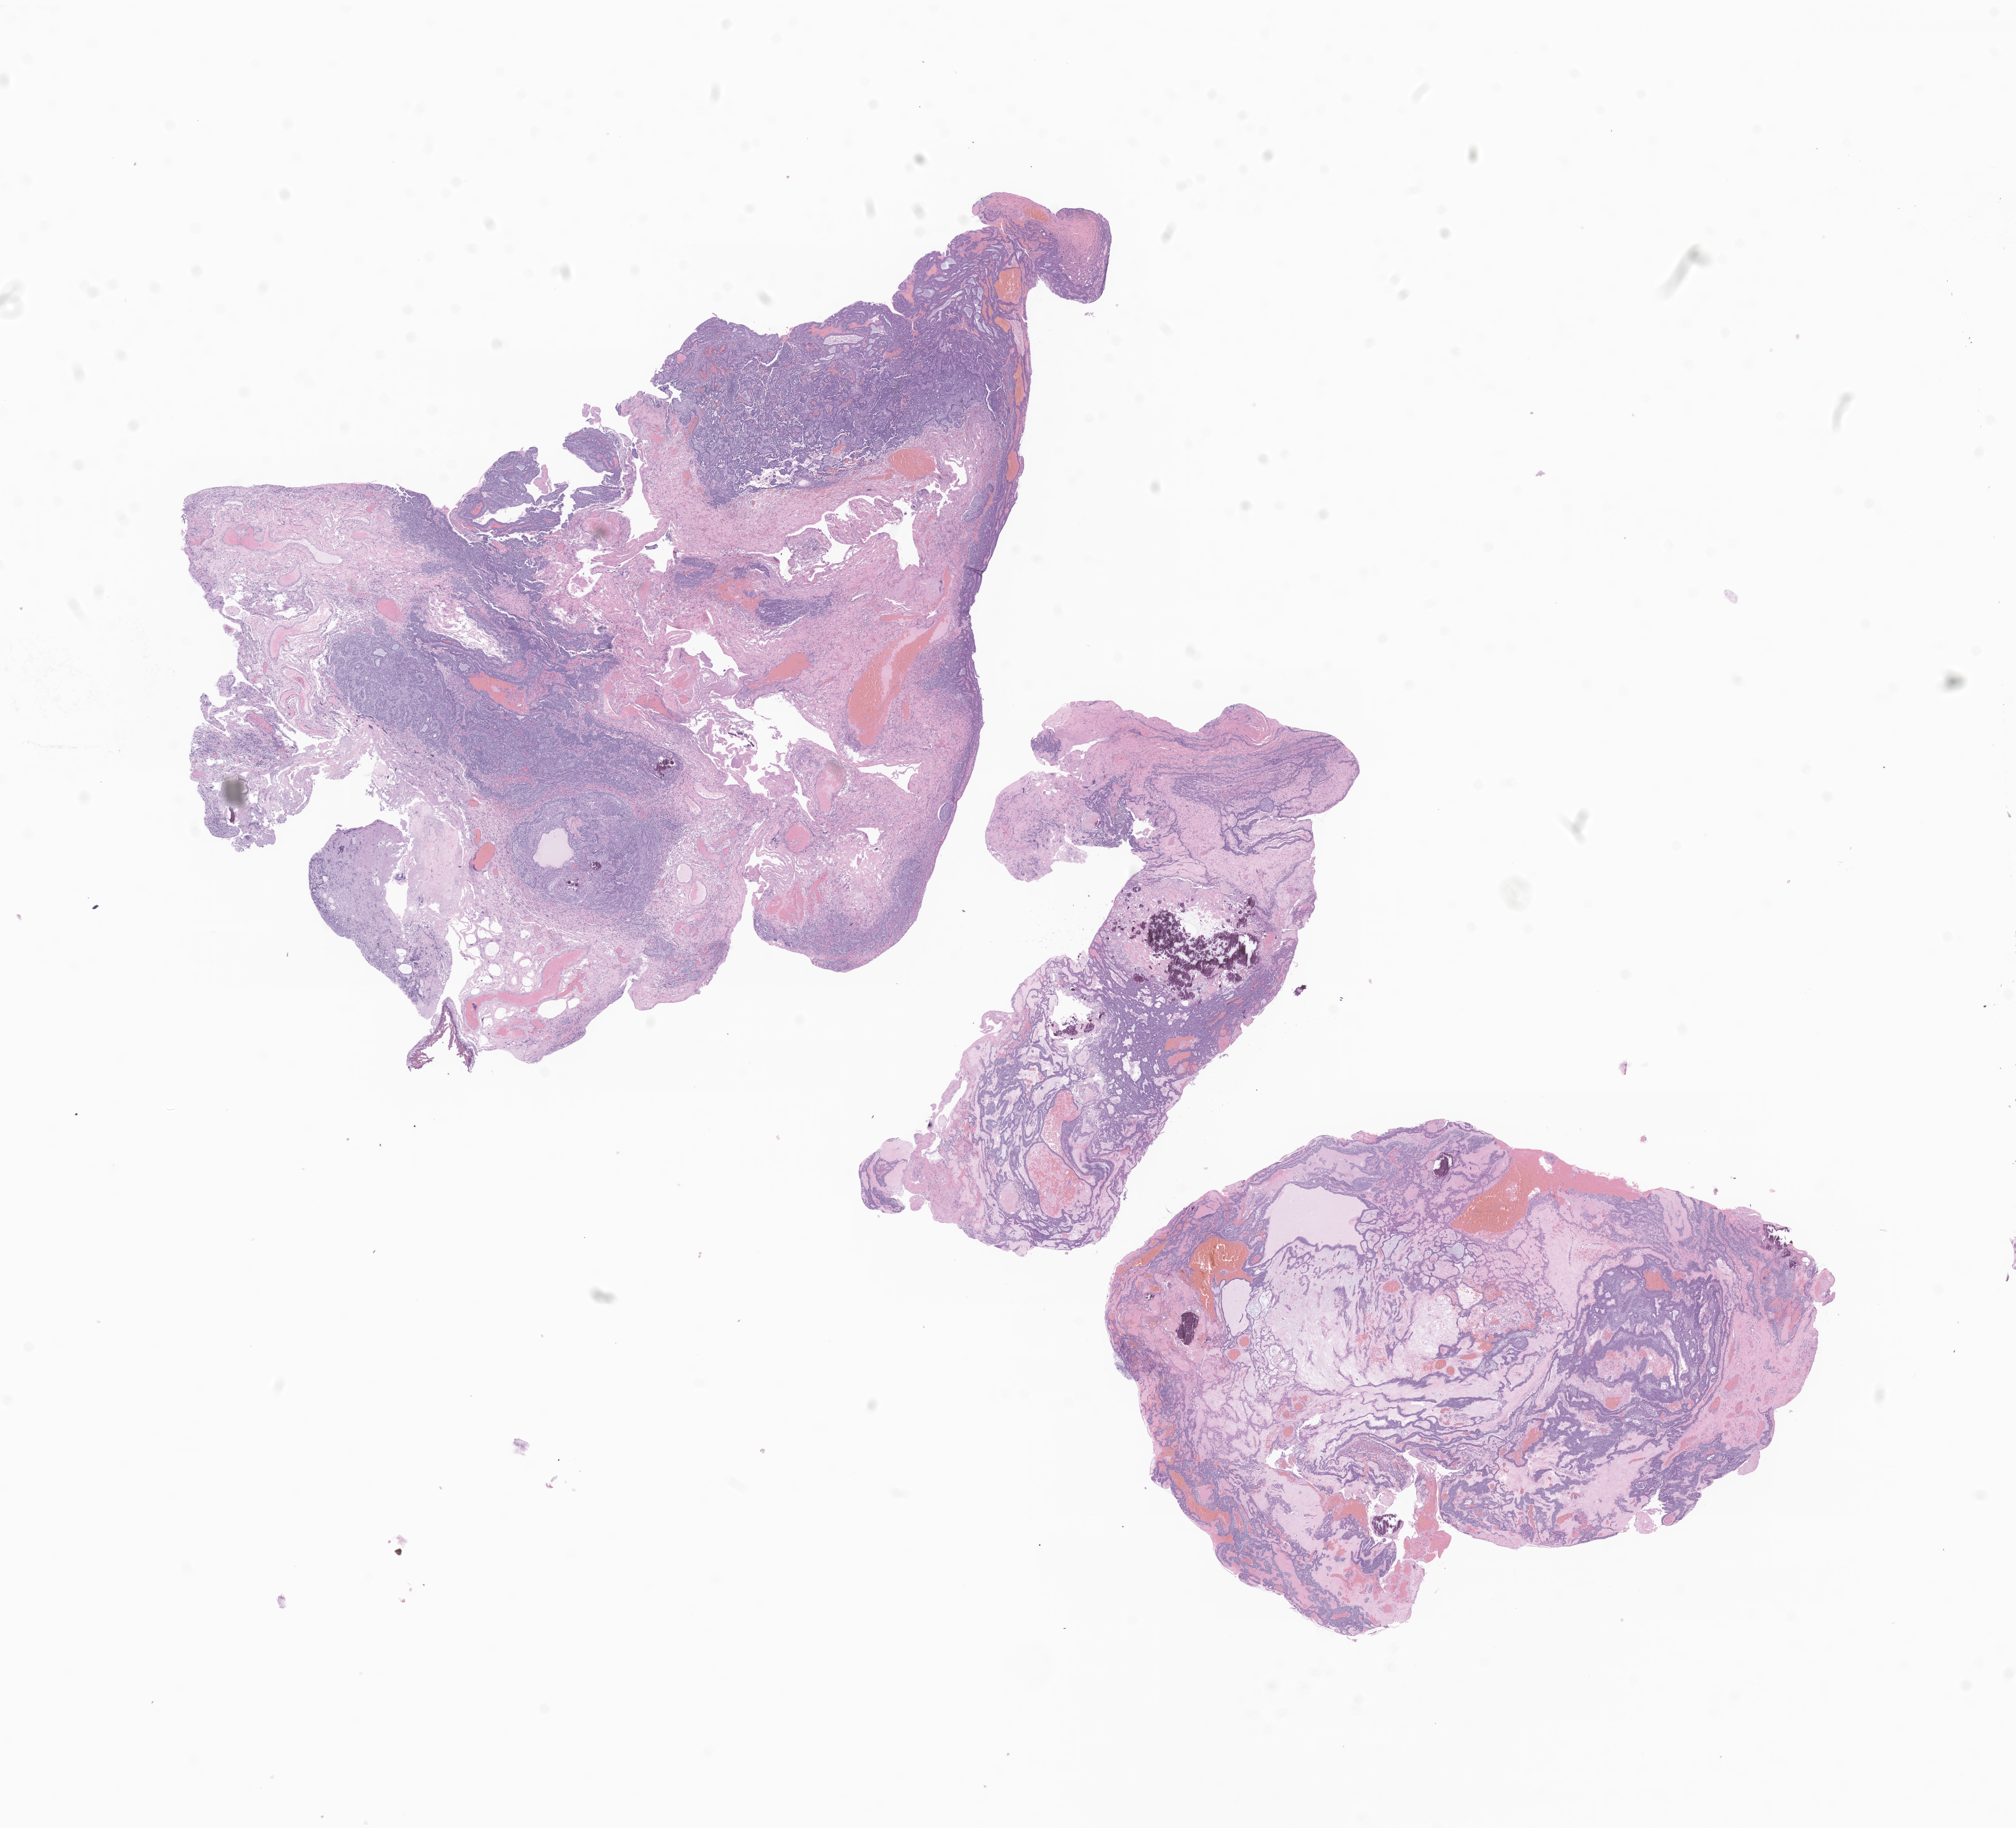
Digitized haematoxylin and eosin-stained section of tumor tissue from the brain stem, whole scanned area (about 20.3 x 18.4 mm) shown as a low-resolution overview, formalin-fixed paraffin-embedded section. Female patient, age 188 months (15 years 8 months).
Diagnosis: Craniopharyngioma, NOS.